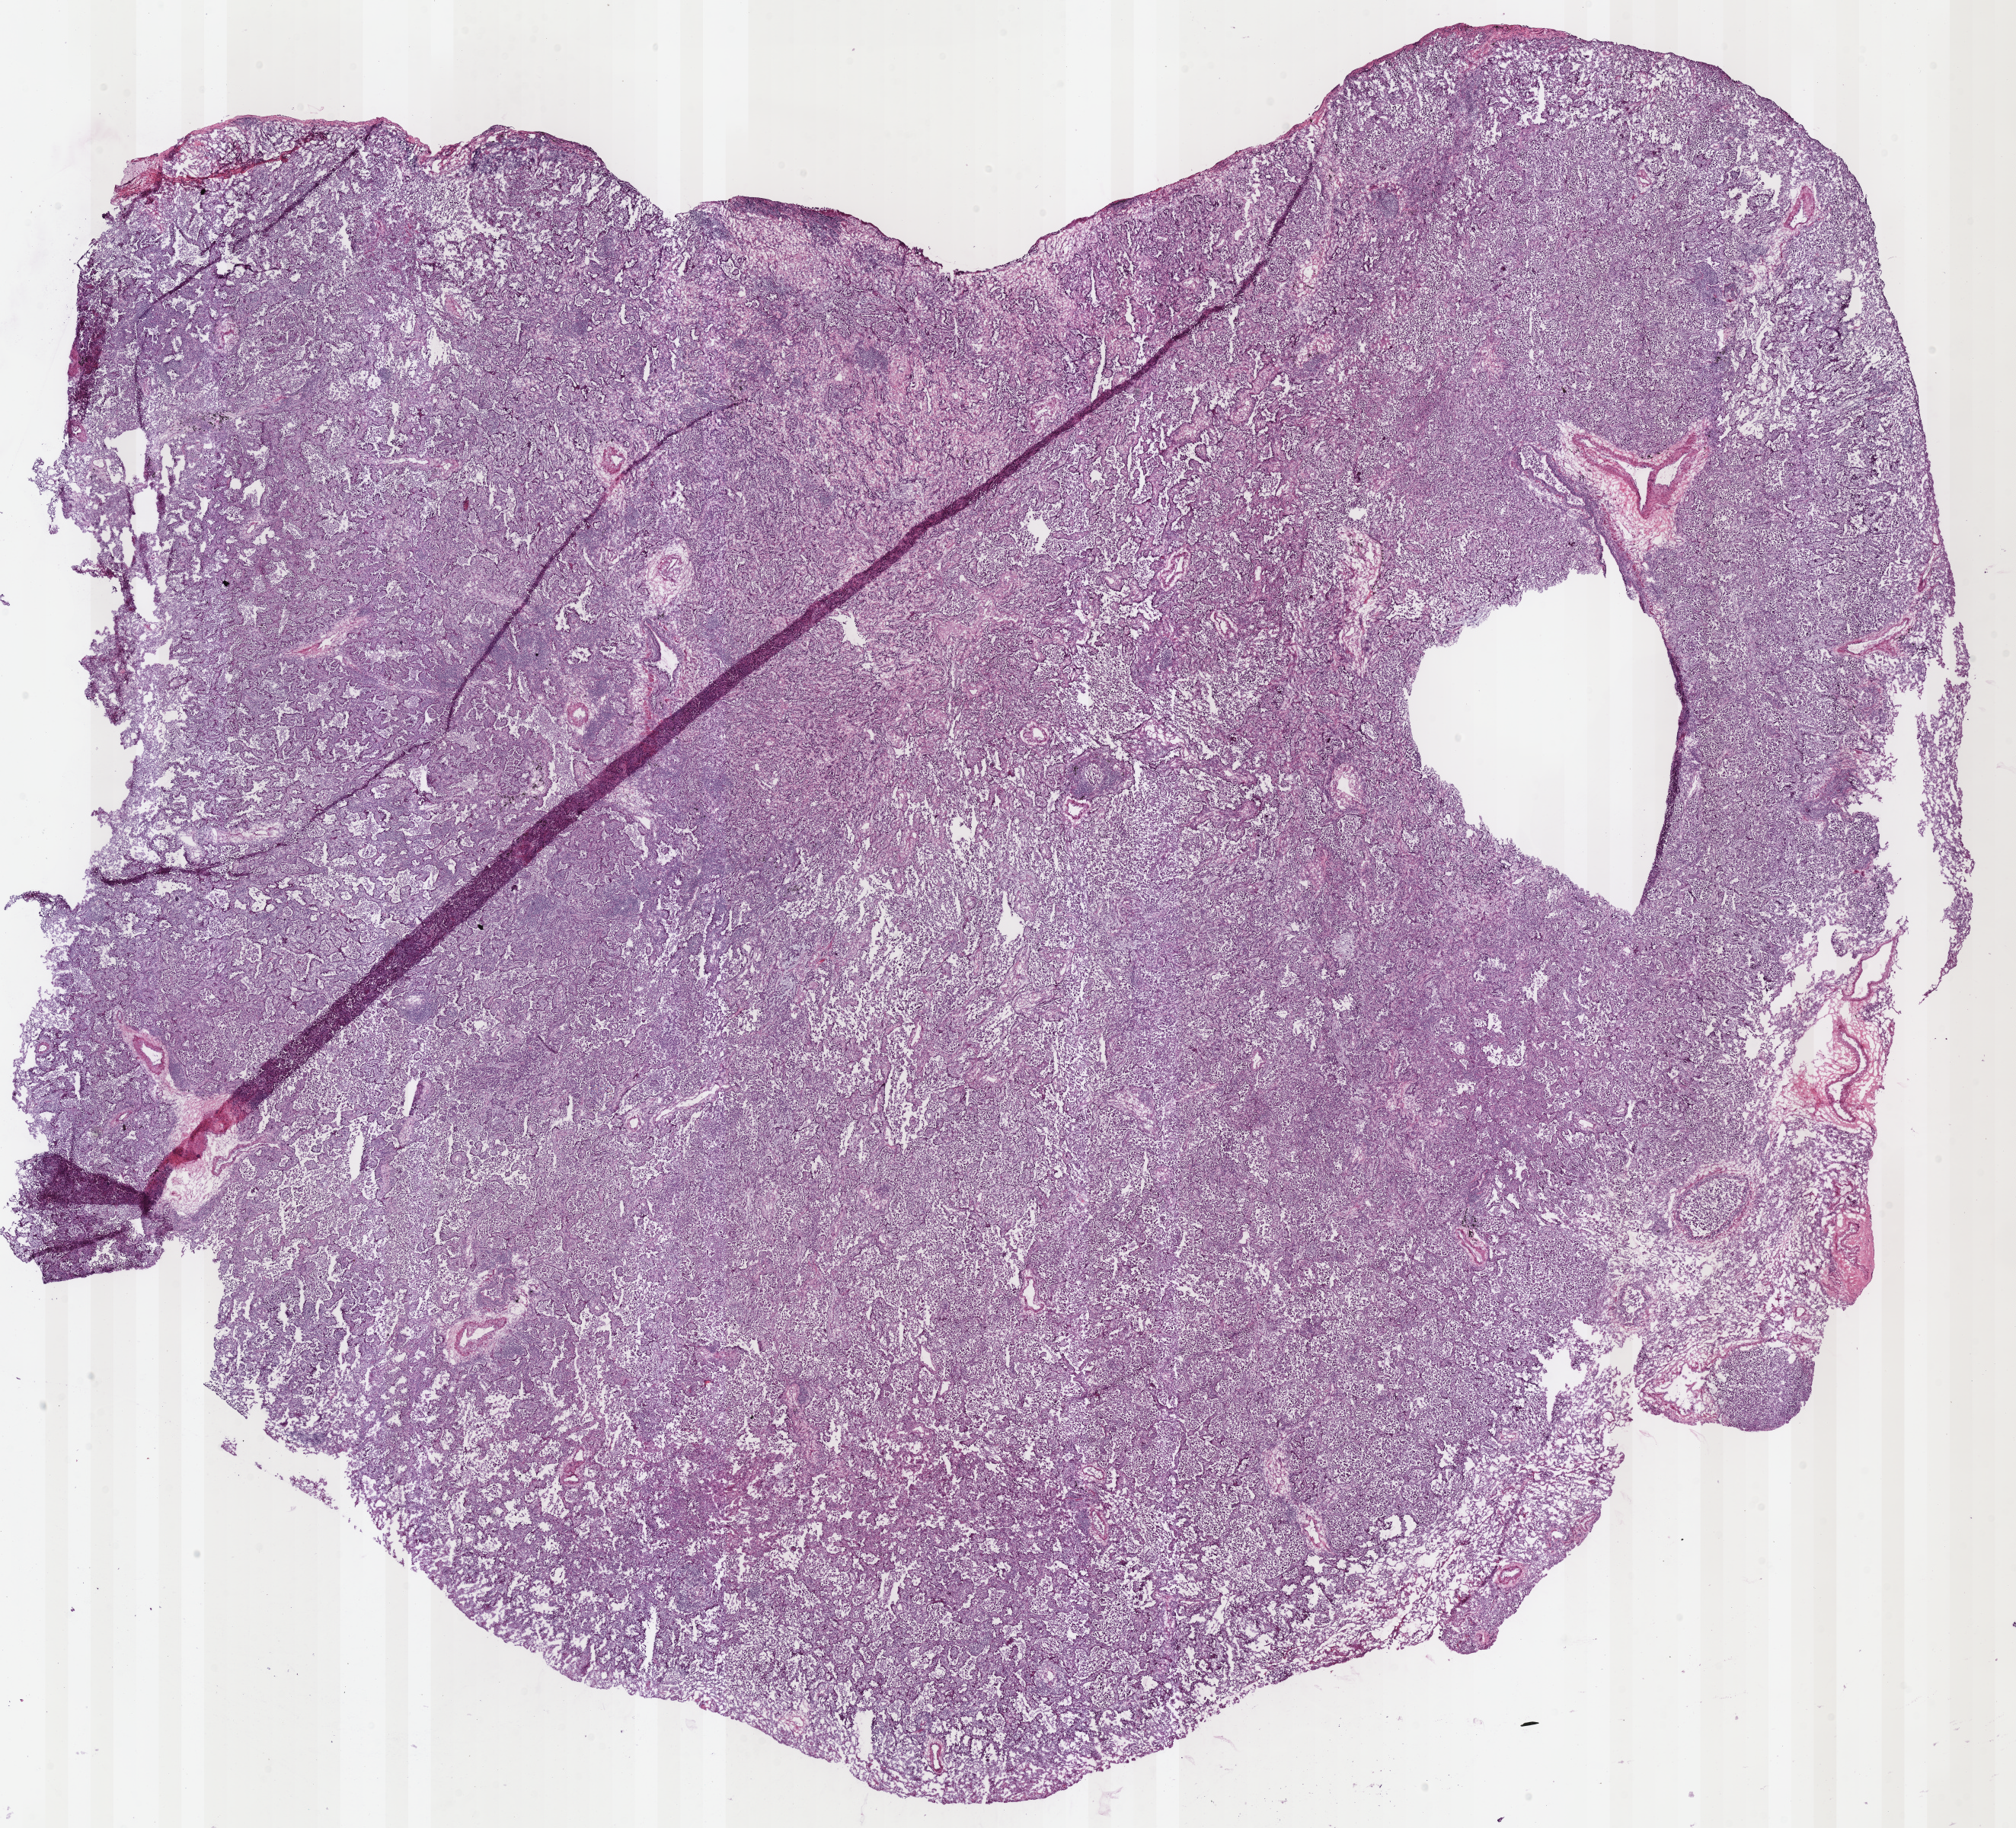
Whole-slide histology image, Hematoxylin and eosin (H&E) stained — shown as a low-resolution overview of the whole scanned area (about 20.9 x 18.9 mm). Frozen section from the bottom of the tissue portion. Lung, primary tumour sample. Female patient; age at initial diagnosis 61 years. Pathologist review of this section (percent, as recorded): tumour cells 100%, tumour nuclei 70%, normal cells 0%, stromal cells 0%, necrosis 0%. Infiltration values recorded for this section: lymphocyte infiltration 12%, monocyte infiltration 0%, neutrophil infiltration 0%.
* AJCC pathologic stage: IA (7th edition)
* pathologic diagnosis: Bronchio-alveolar carcinoma, mucinous (lower lobe, lung)